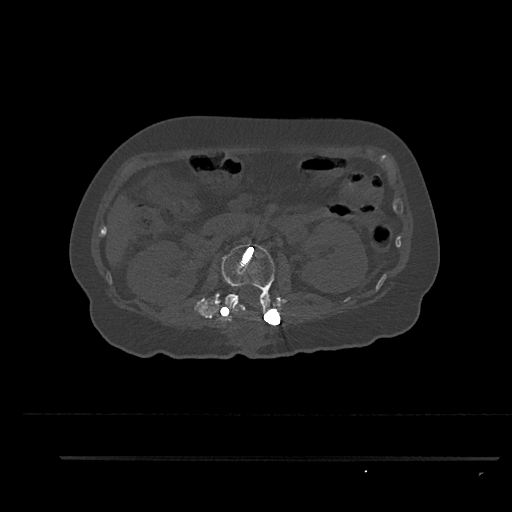
CT including the spine, one axial slice. Slice 179 of 797 in the series (ordered by position). Reconstruction kernel Br40s/3. Bone window (W 1800 / L 400 HU). 0.5 mm slice thickness. 512 × 512 image matrix, field of view 408 × 408 mm. Patient: female, 44 years. From the clinical record (not read from this slice): primary cancer: renal; vertebrae with lytic lesions (as recorded): L1.
Structures marked on this image (semi-automatically segmented with operator editing):
- L2 vertebra: bounding box <219,241,276,322> (left, top, right, bottom; pixels)